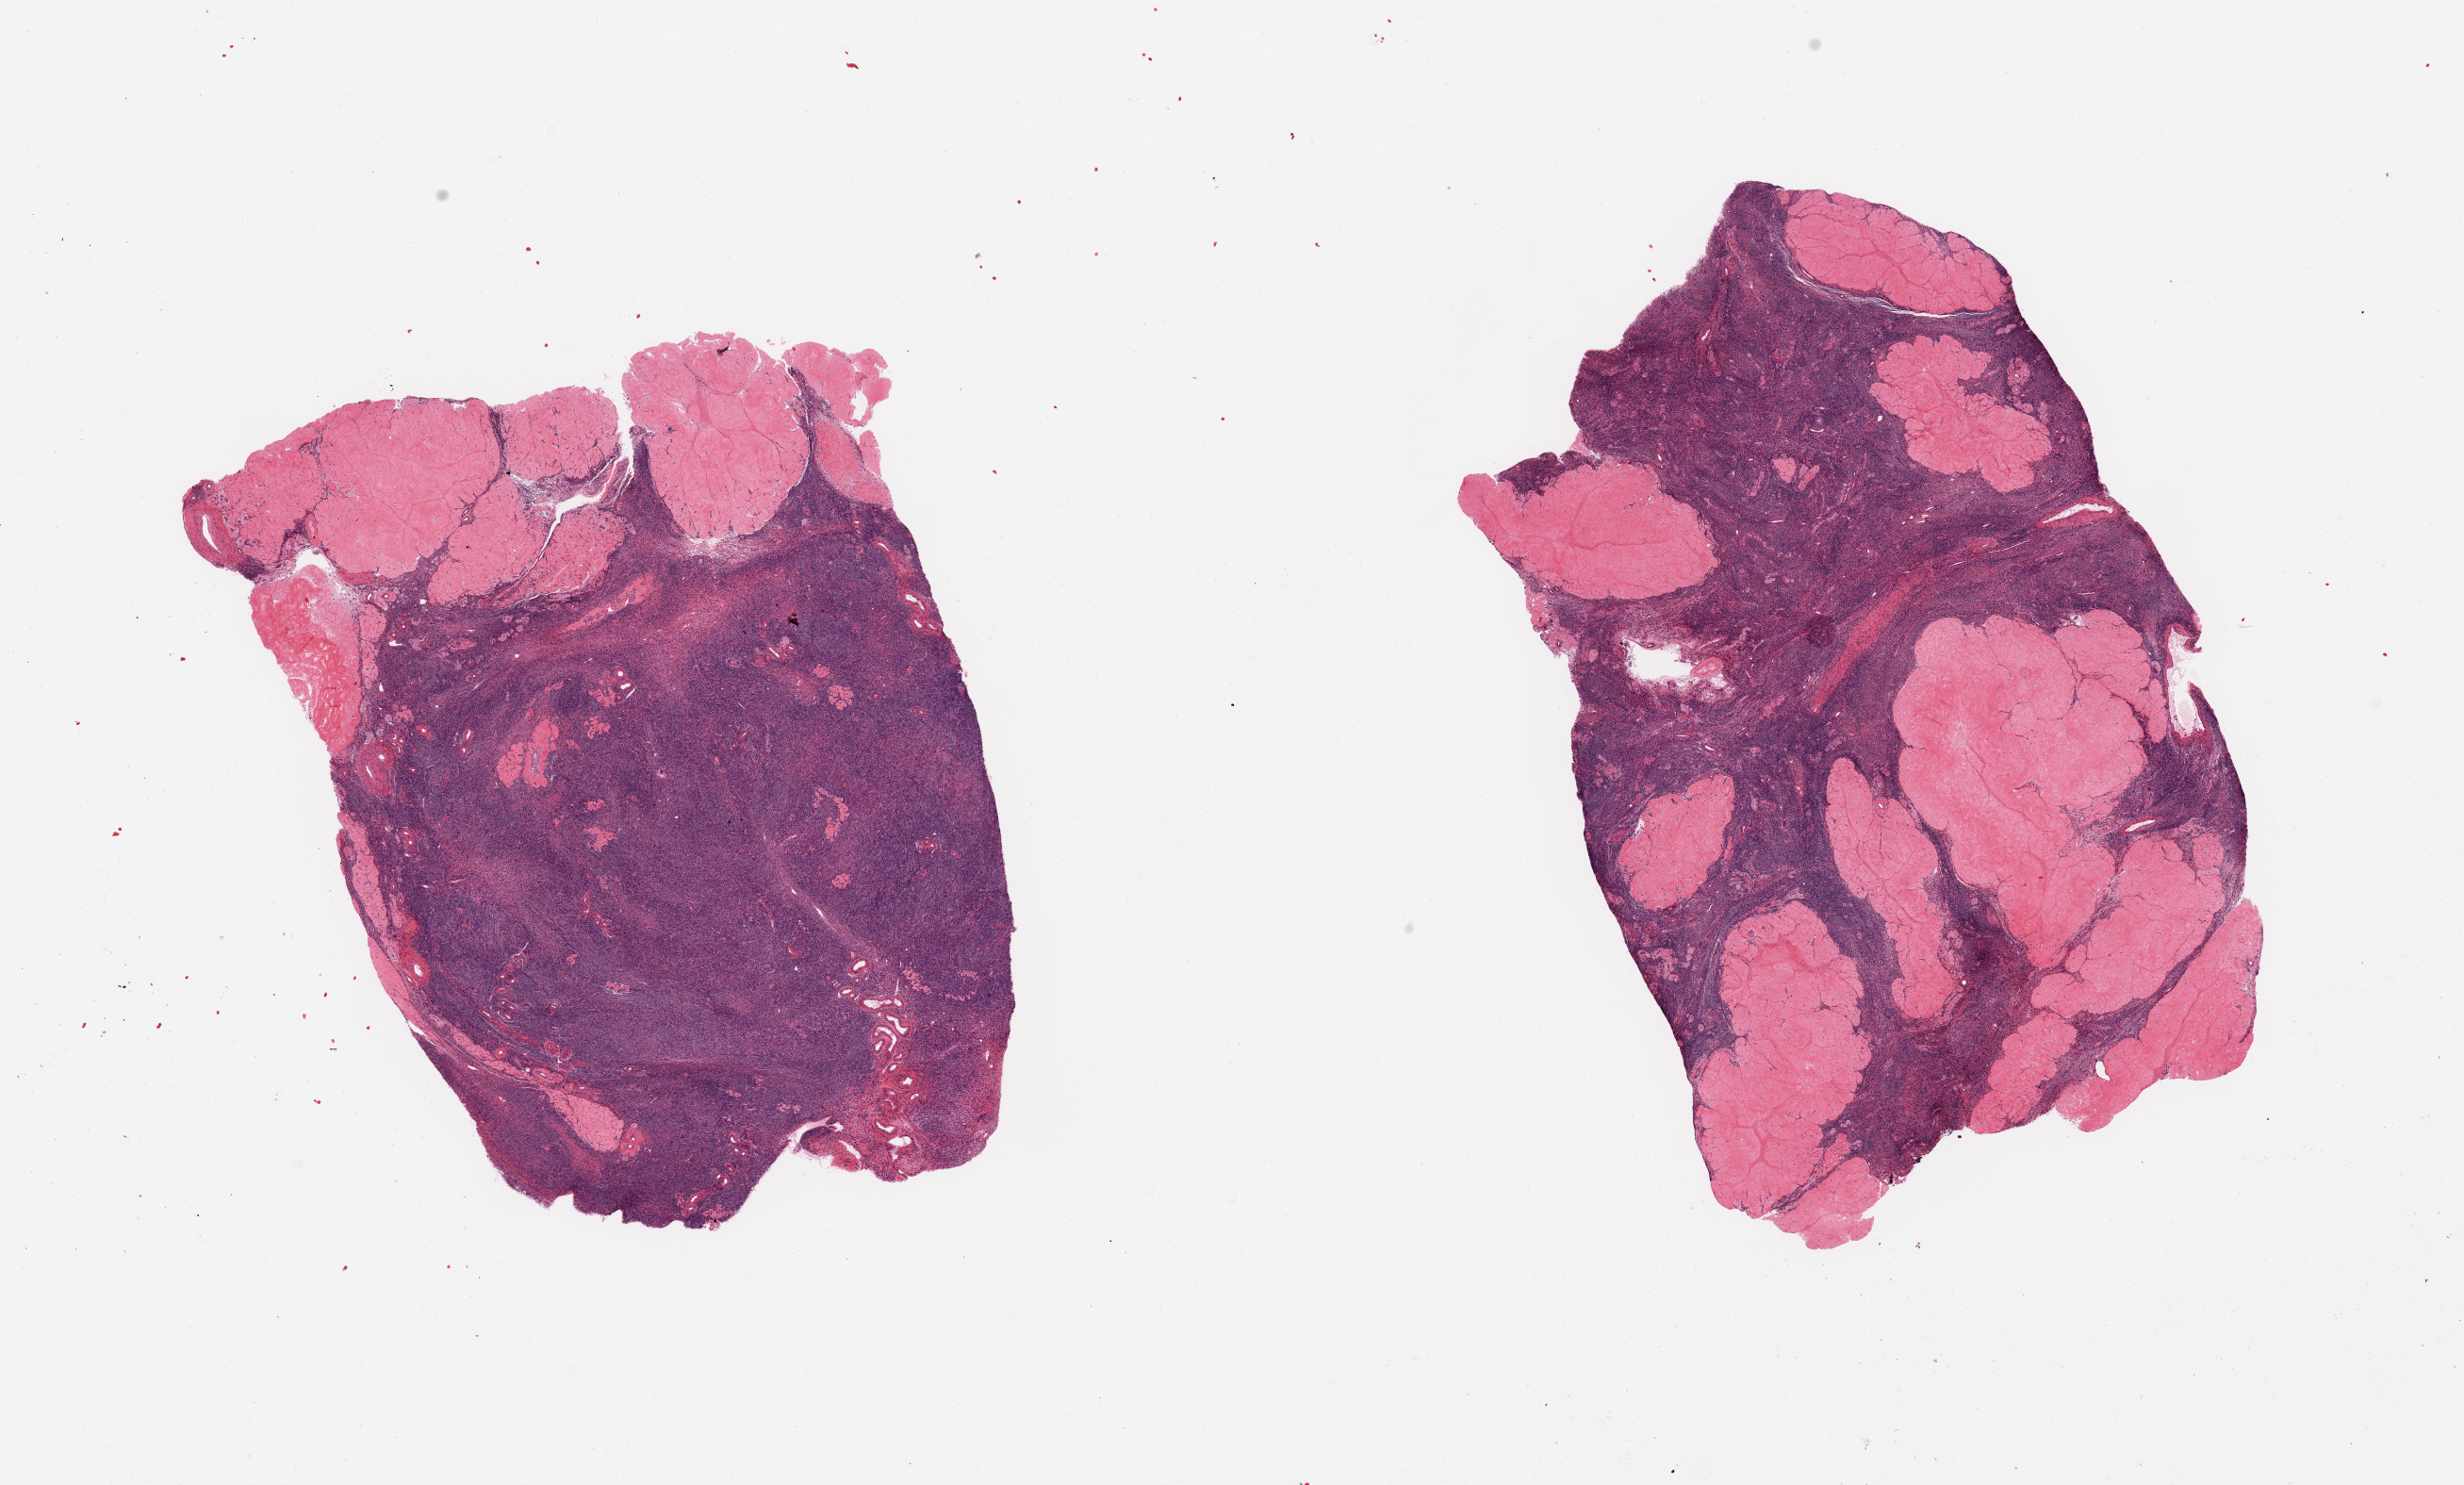
Whole-slide image, hematoxylin and eosin (H&E) stain, brightfield — shown as a low-resolution overview of the whole scanned area (about 20.7 x 12.5 mm, acquisition: 20x scan). PAXgene-fixed, paraffin-embedded tissue. Target tissue: ovary. Donor tissue sample. Donor: female.
Pathologist's review note for this sample: 2 pieces, post menopausal-type atrophy, prominent corproa albicantia.